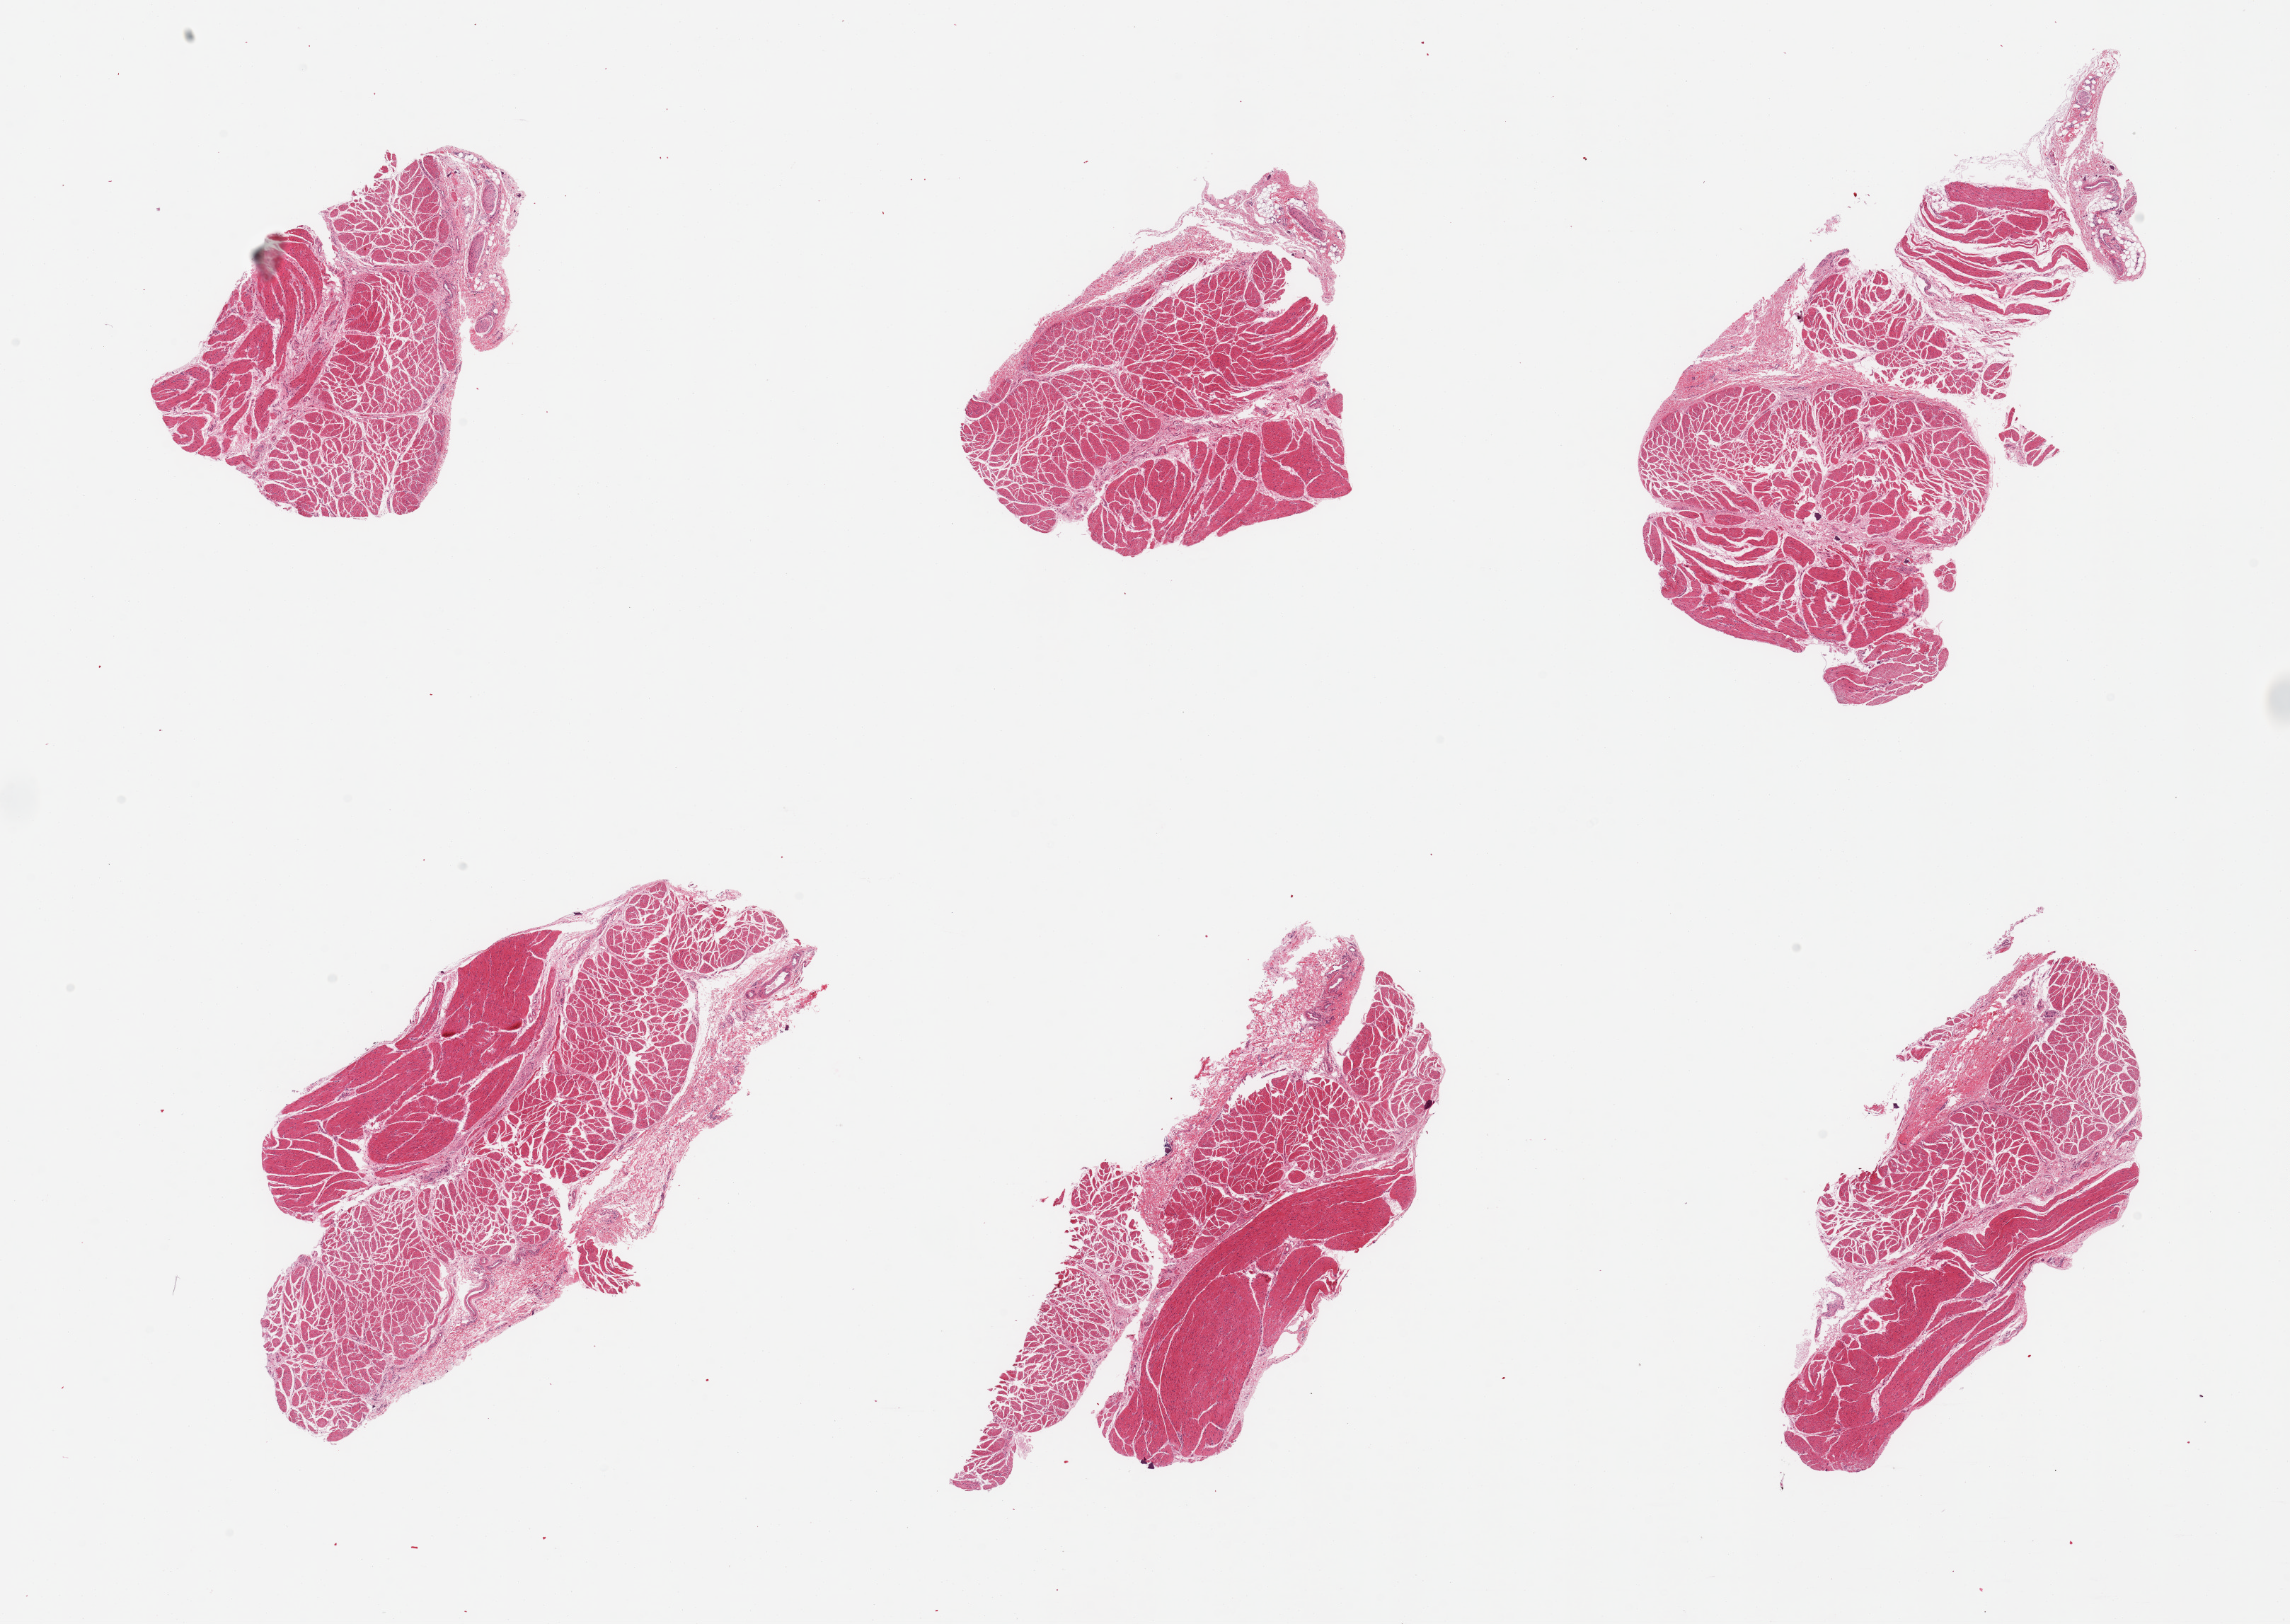
Whole-slide image, H&E stain, a low-resolution overview of the entire scanned area, about 25.6 x 18.2 mm (slide scanned at 20x). PAXgene-fixed paraffin-embedded (PFPE) section. Target tissue: esophageal muscle. Tissue donor sample. Donor: male.
Reviewer comment on this tissue sample: 6 pieces; target muscularis.